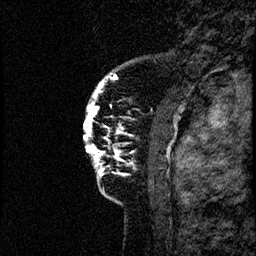
Breast MRI (dynamic contrast-enhanced), one sagittal slice. Slice 11 of 60 in the series (ordered by position). Dynamic contrast-enhanced study with each time point stored as its own series, time point 2 of 4 at this slice position (early post-contrast, ordered by acquisition time). 1.5 T. TE 4.2 ms, TR 17.6 ms. 256 × 256 image matrix, field of view 200 × 200 mm. Patient: female, 40 years. Case-level facts recorded for this patient, not image findings: setting: breast cancer imaged before/during neoadjuvant chemotherapy; receptor status: HER2-positive.
Structures marked on this image (semi-automatically segmented with operator editing):
- analysis volume of interest (the breast-tissue region the enhancement analysis was run in; not a lesion): box from (x=80, y=55) to (x=185, y=206) px
- tumour enhancement mask (voxels above the 100 % enhancement threshold inside the analysis volume of interest): (x=83, y=73)–(x=118, y=174)